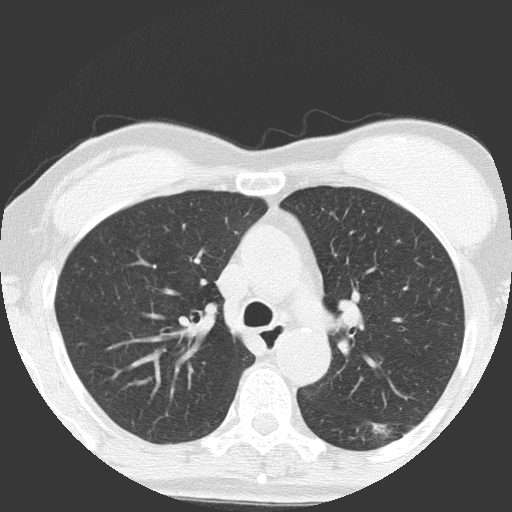
Chest CT (low-dose screening protocol), one axial image. Baseline screening round. Lung window (W 1500 / L -600 HU). 2 mm slice thickness. Lung (sharp) reconstruction kernel (FC51). Slice 48 of 149 in the series. Female participant, aged 64 years at enrolment.
- Expert reader's lesion annotation, bounding box (x1, y1, x2, y2) in pixels: (329, 401, 418, 470).
- Reader record for this screening exam (exam-level; its link to the box is not recorded): non-calcified nodule or mass ≥4 mm, right upper lobe, 4 × 4 mm, poorly defined margins, ground glass attenuation.
- Note: the box lies in the patient's left hemithorax on this image, whereas the reader's record names the right lung; they may be different findings.
- Later outcome: lung cancer diagnosed 932 days after this screen (after the third annual screen) — adenocarcinoma, NOS, left lower lobe, moderately differentiated (G2), stage IA (AJCC 6th edition), 17 mm at pathology.